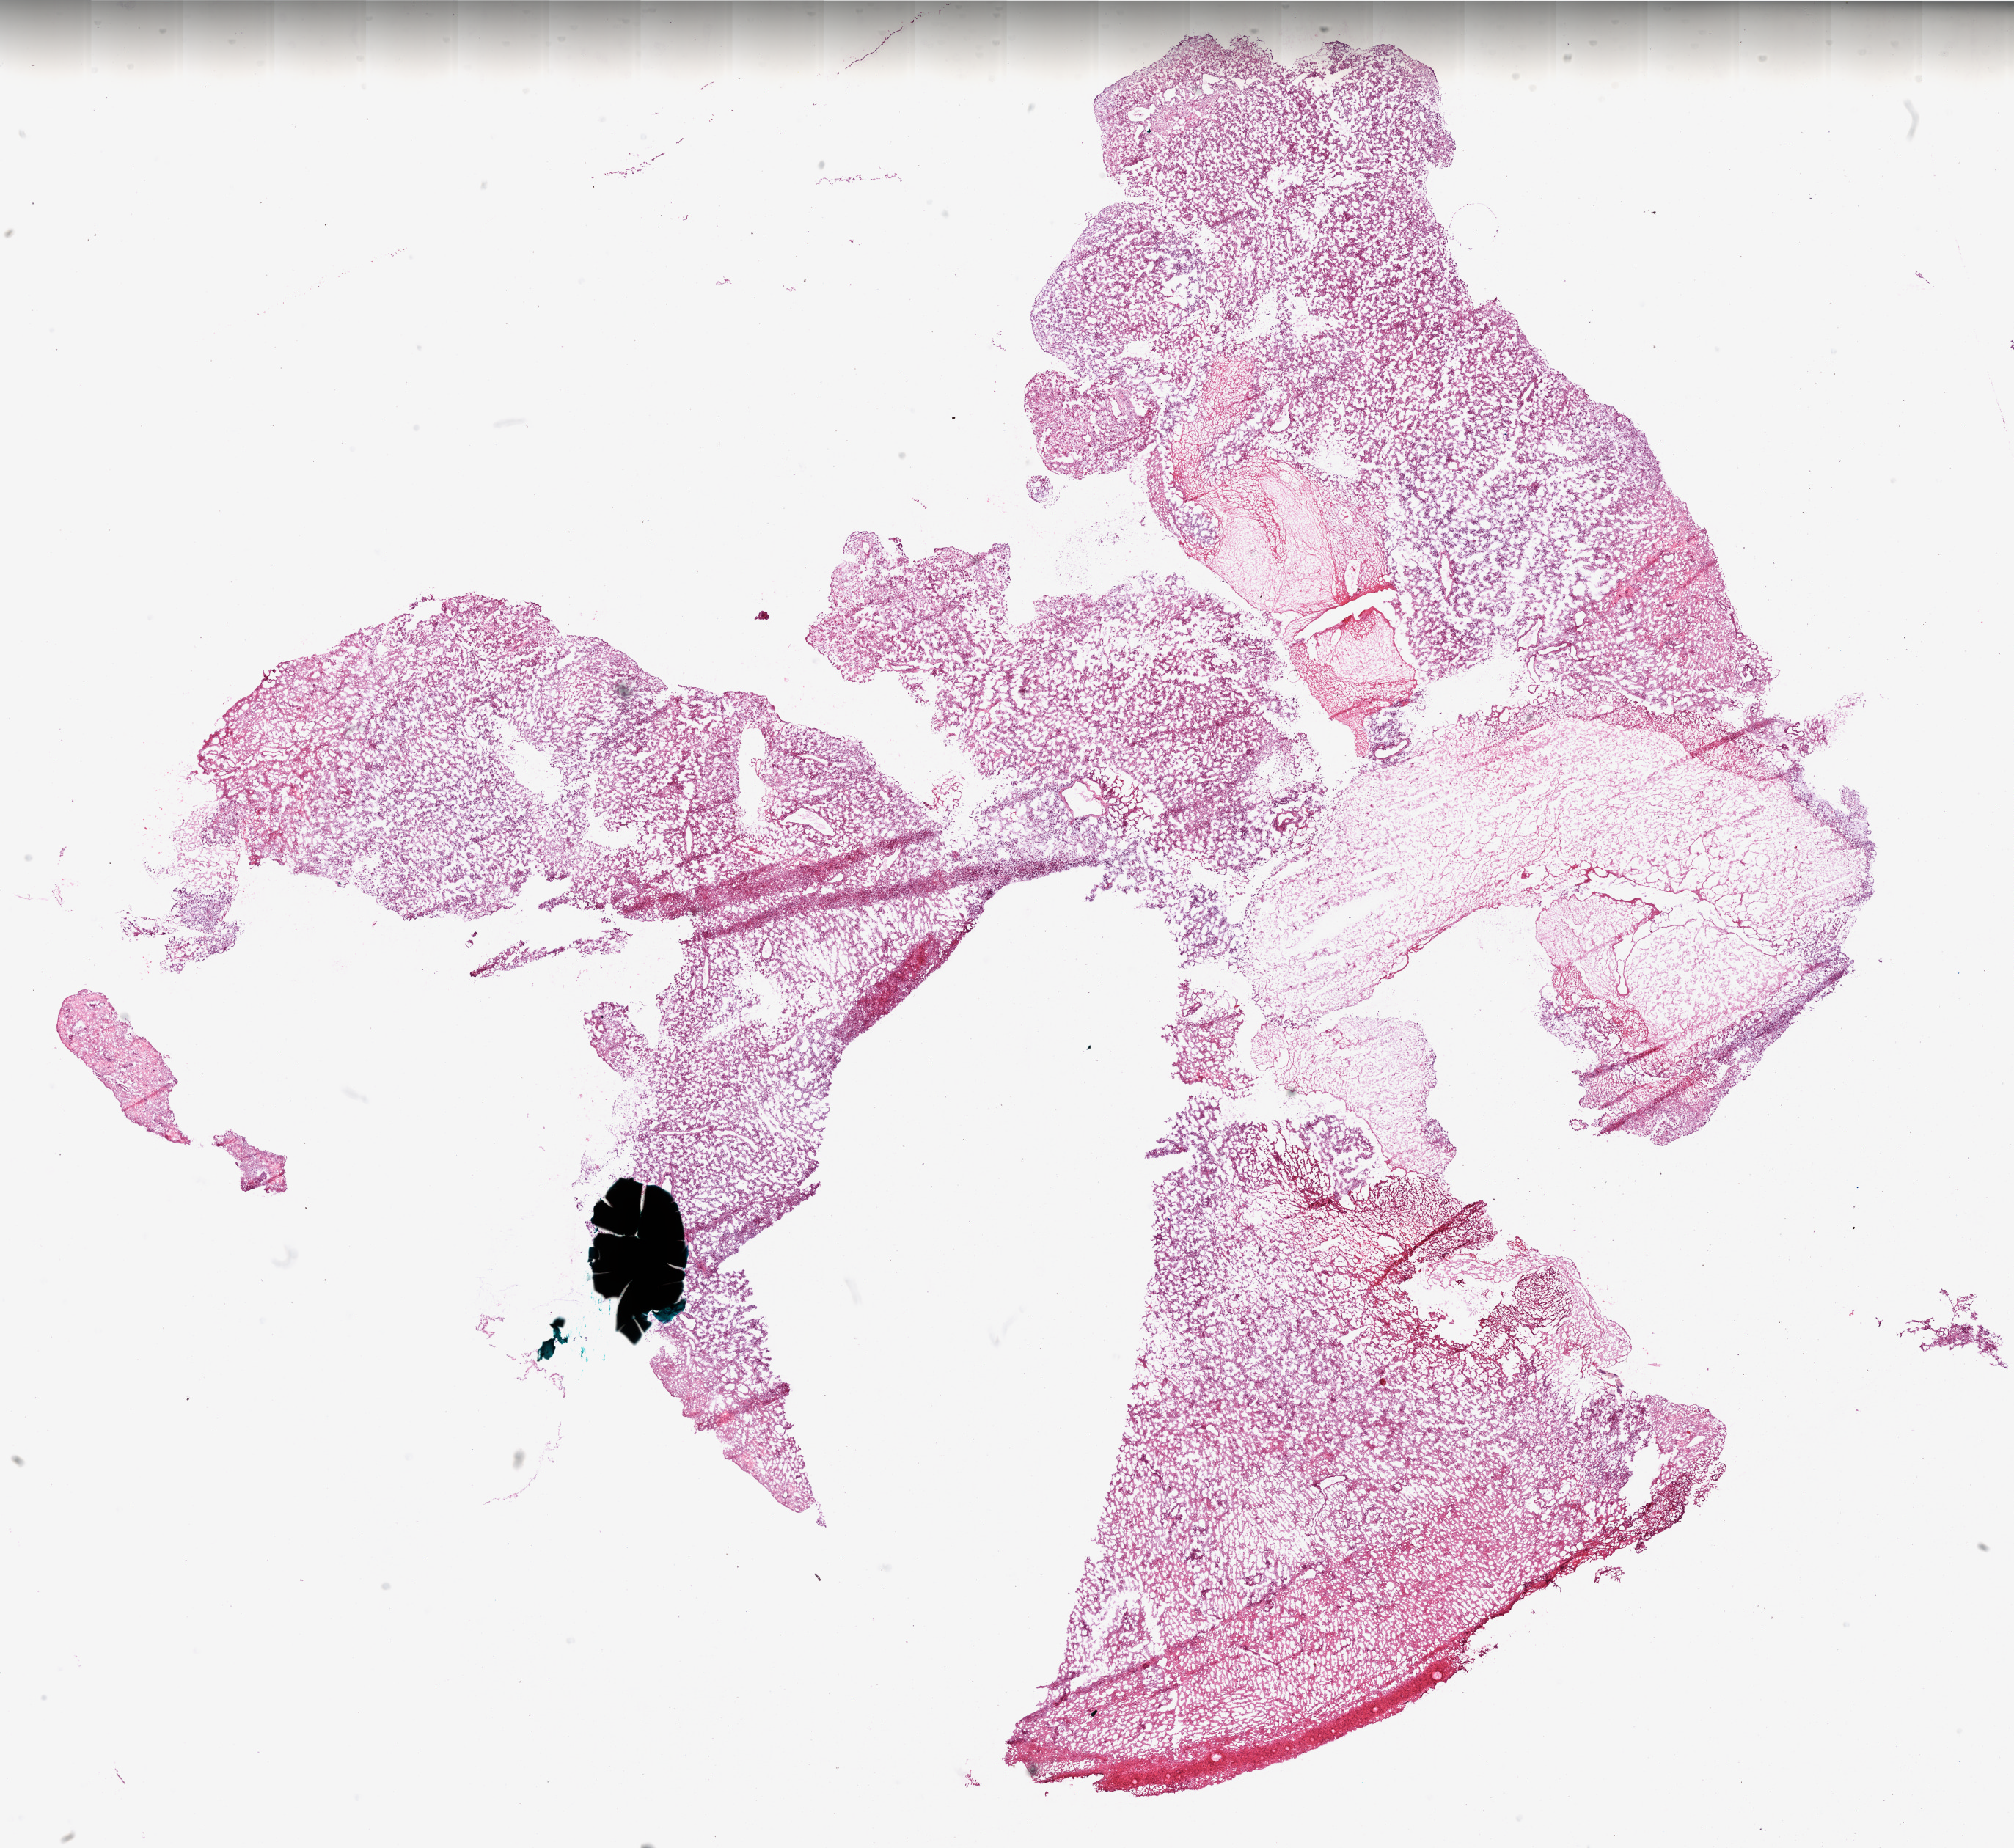
H&E whole-slide image — a low-resolution overview of the entire scanned area, about 22.0 x 20.2 mm (from a 20x scan). Frozen section. Primary tumour sample from the brain. Male patient; age at initial diagnosis 48 years. Slide review estimates, as recorded: tumour cells 70%, tumour nuclei 95%, normal cells 0%, stromal cells 5%, necrosis 25%. Infiltration values recorded for this section: lymphocyte infiltration 0%.
Pathologic diagnosis: Glioblastoma.